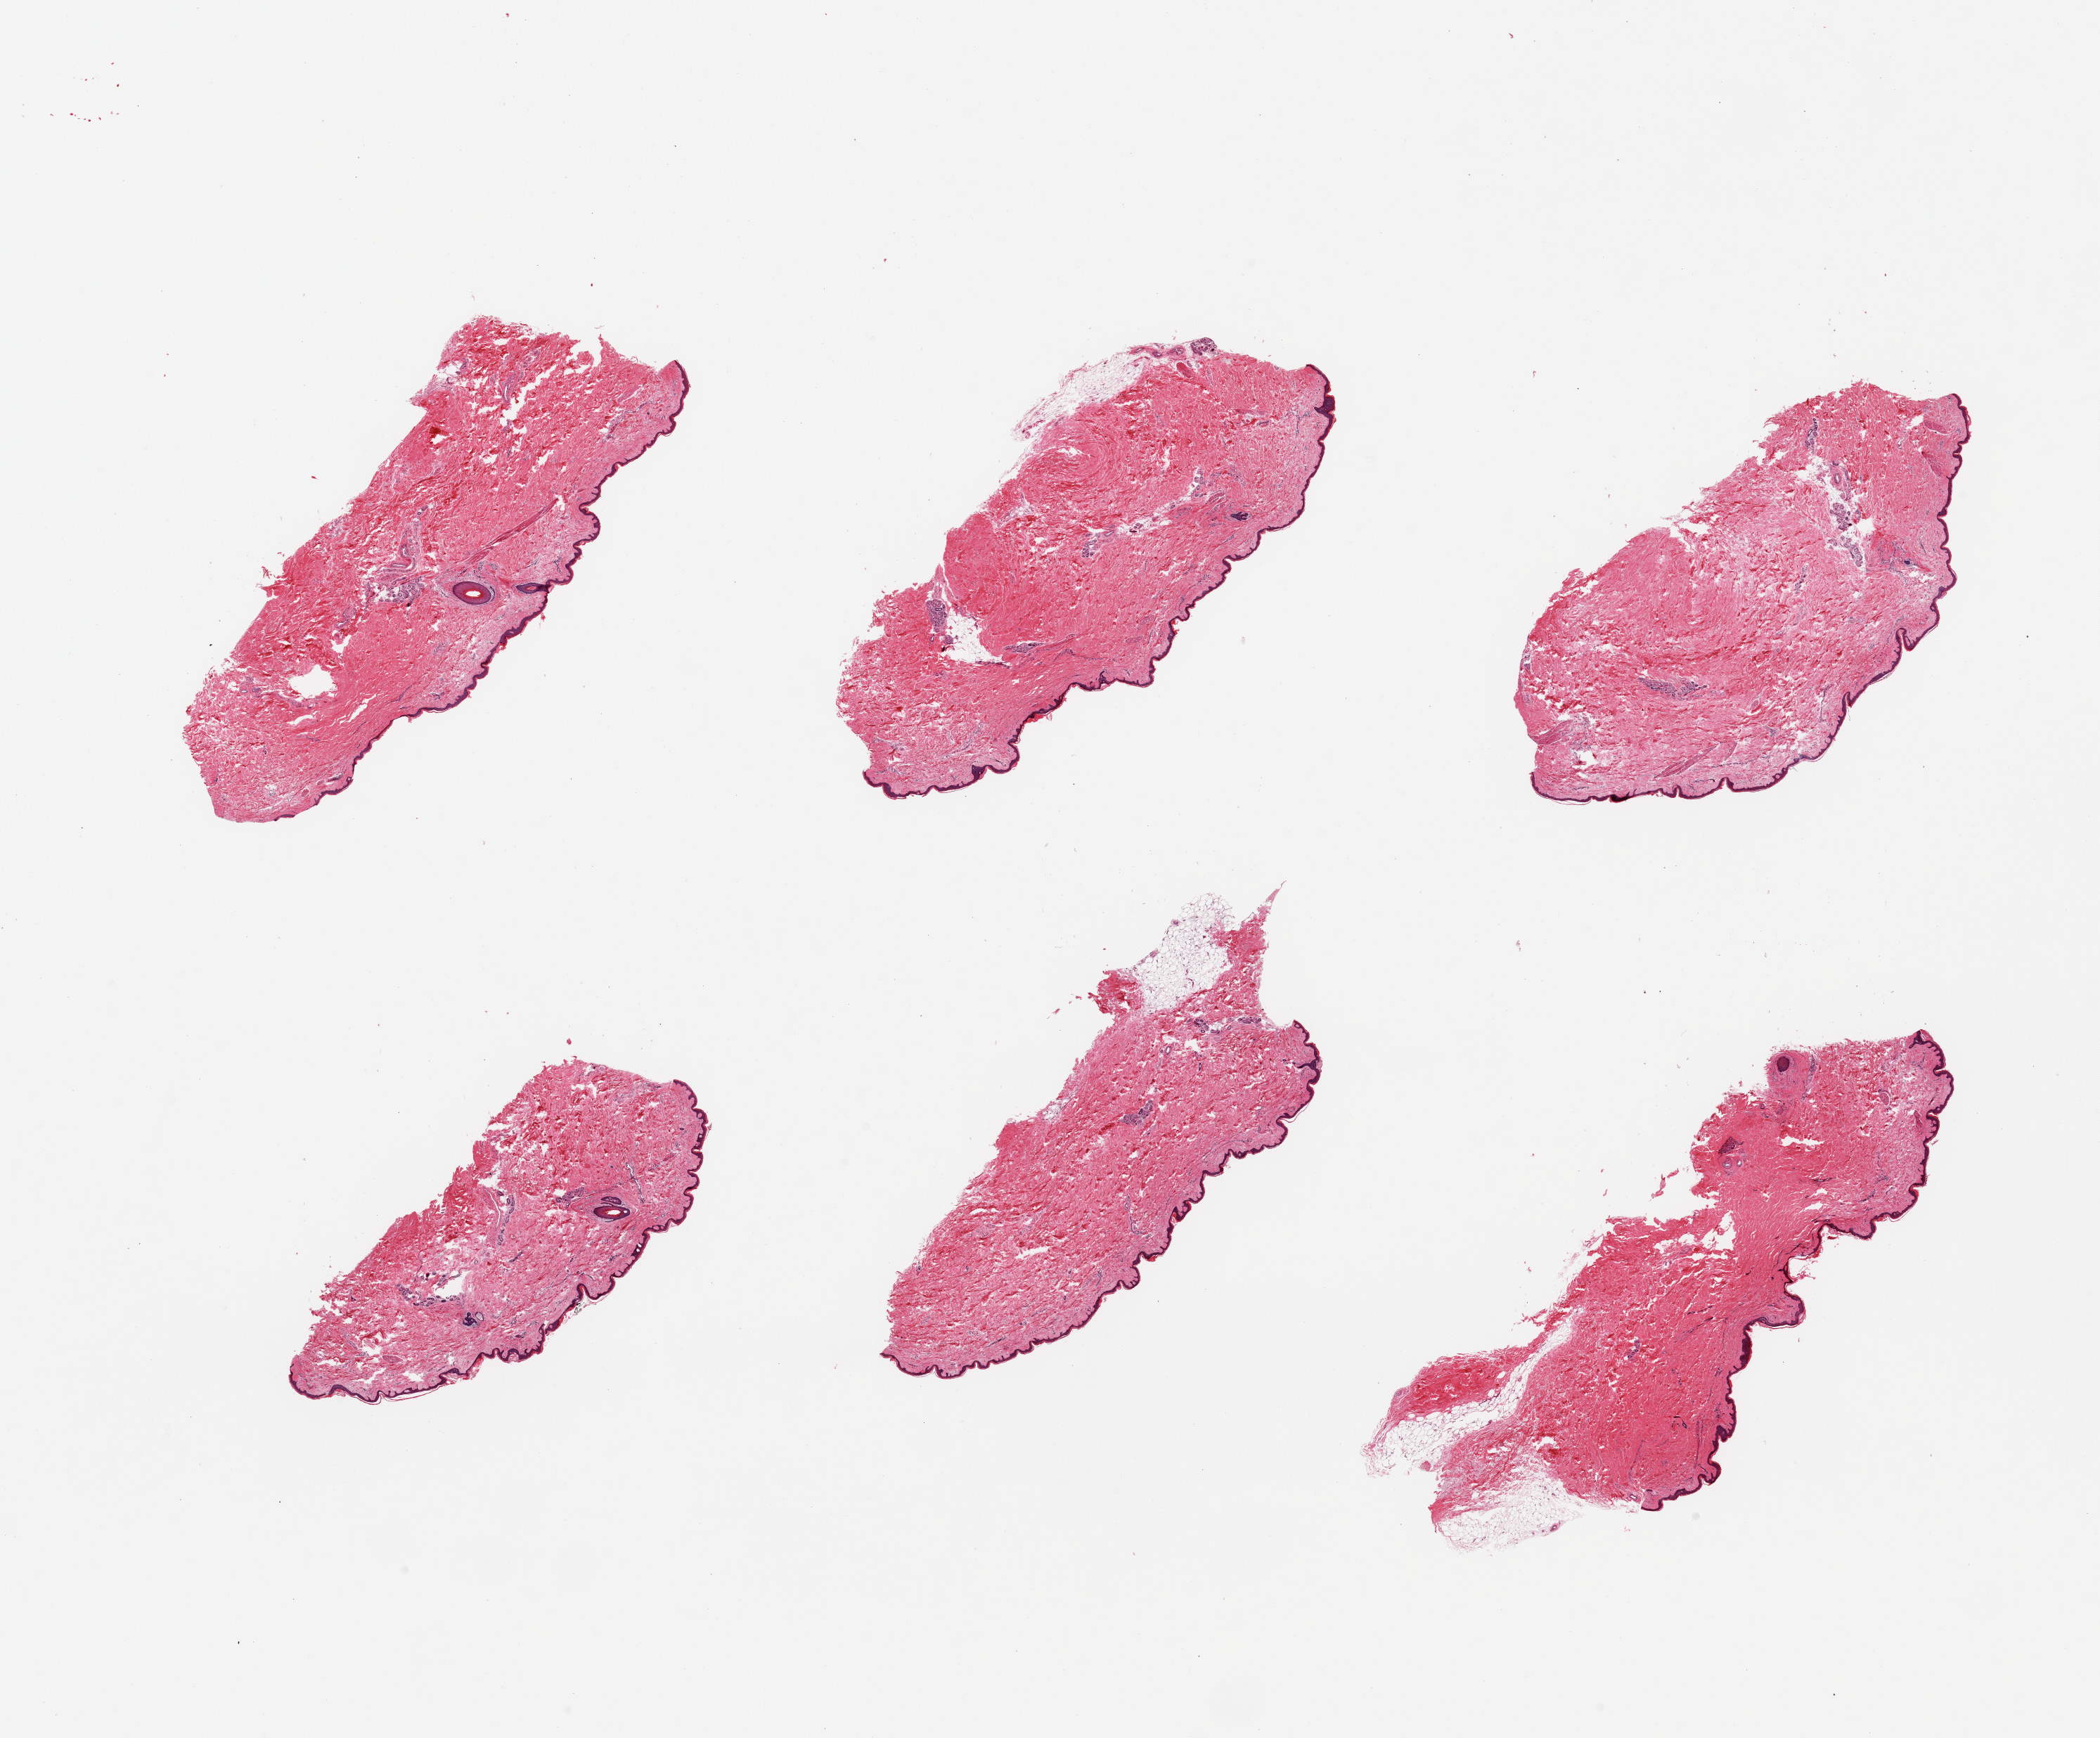
Digitized hematoxylin and eosin (H&E)-stained section — whole scanned area (about 23.6 x 19.6 mm) shown as a low-resolution overview, PAXgene-fixed paraffin-embedded (PFPE) section, section of skin of lower leg (target tissue), donor tissue sample. Donor: male.
• pathologist's review note for this sample: 6 pieces; well trimmed; minimal dermal fat